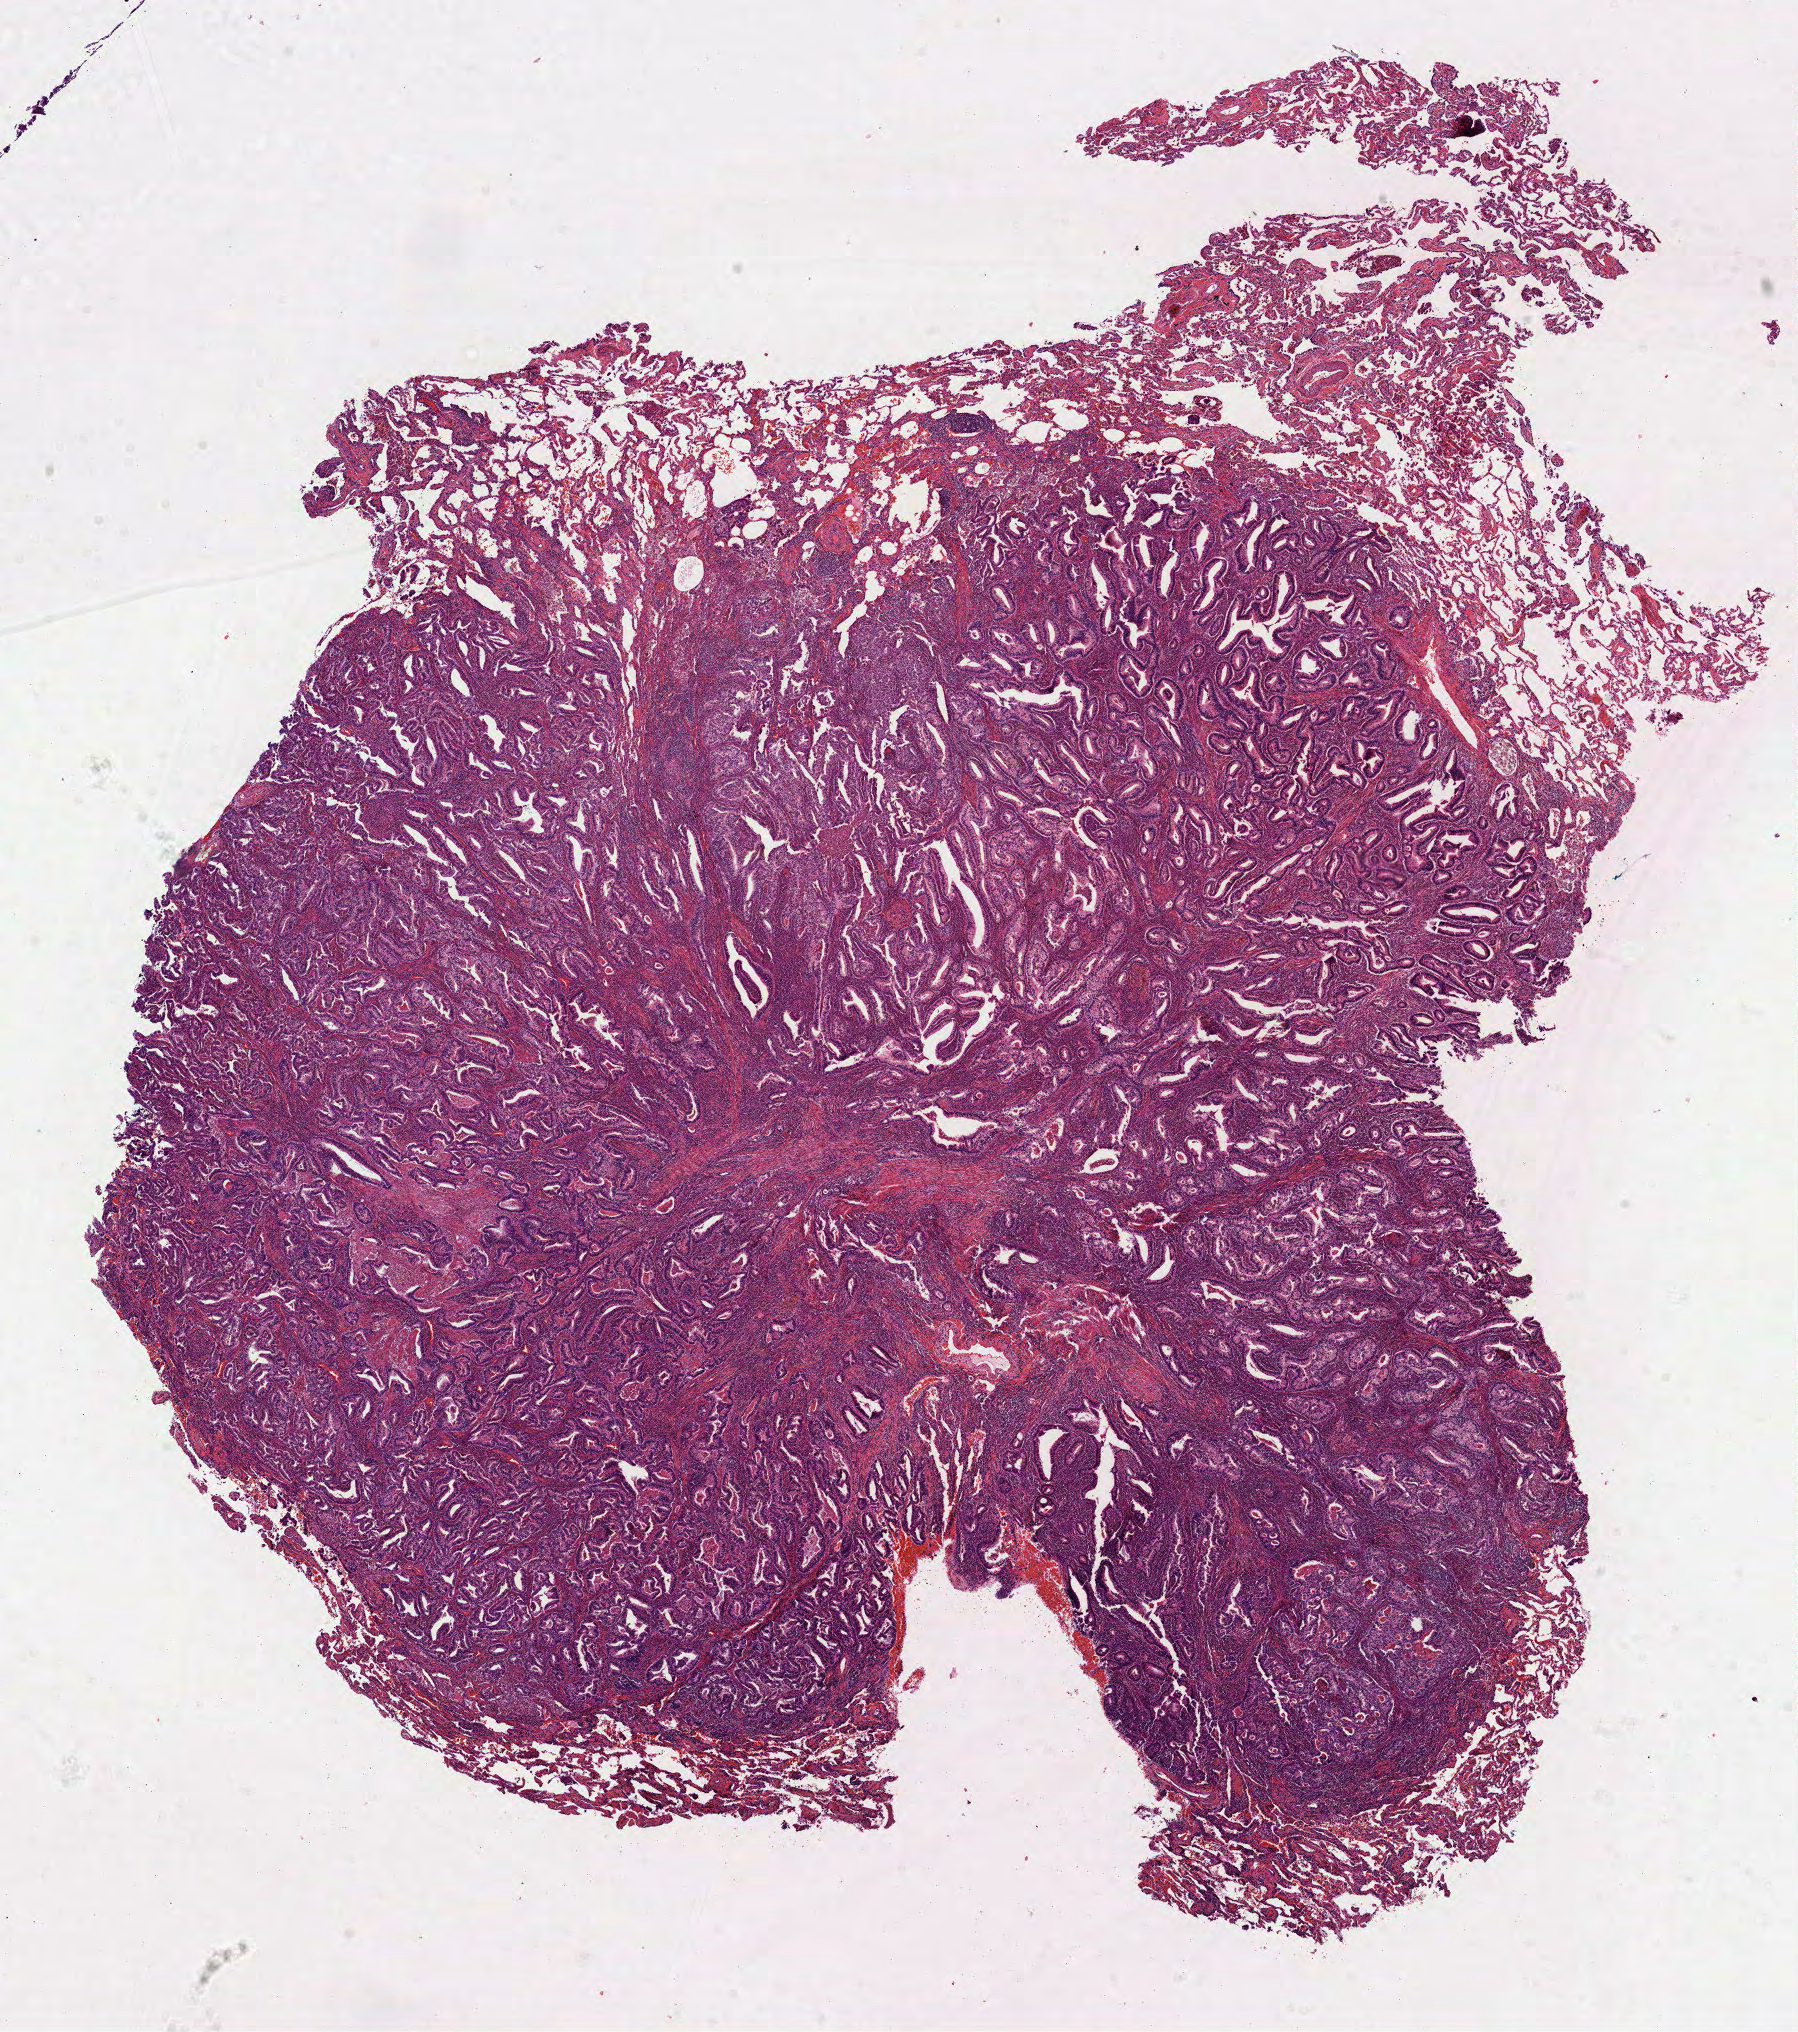
H&E whole-slide image, low-resolution overview of the scanned area, about 14.5 x 16.4 mm (from a 40x scan). Formalin-fixed paraffin-embedded (FFPE) diagnostic section. Lung, primary tumour sample. Female, age 51 years at initial diagnosis.
• TNM: T4 N0 M0
• histologic diagnosis: Bronchiolo-alveolar carcinoma, non-mucinous
• AJCC pathologic stage: IIIB (6th edition)